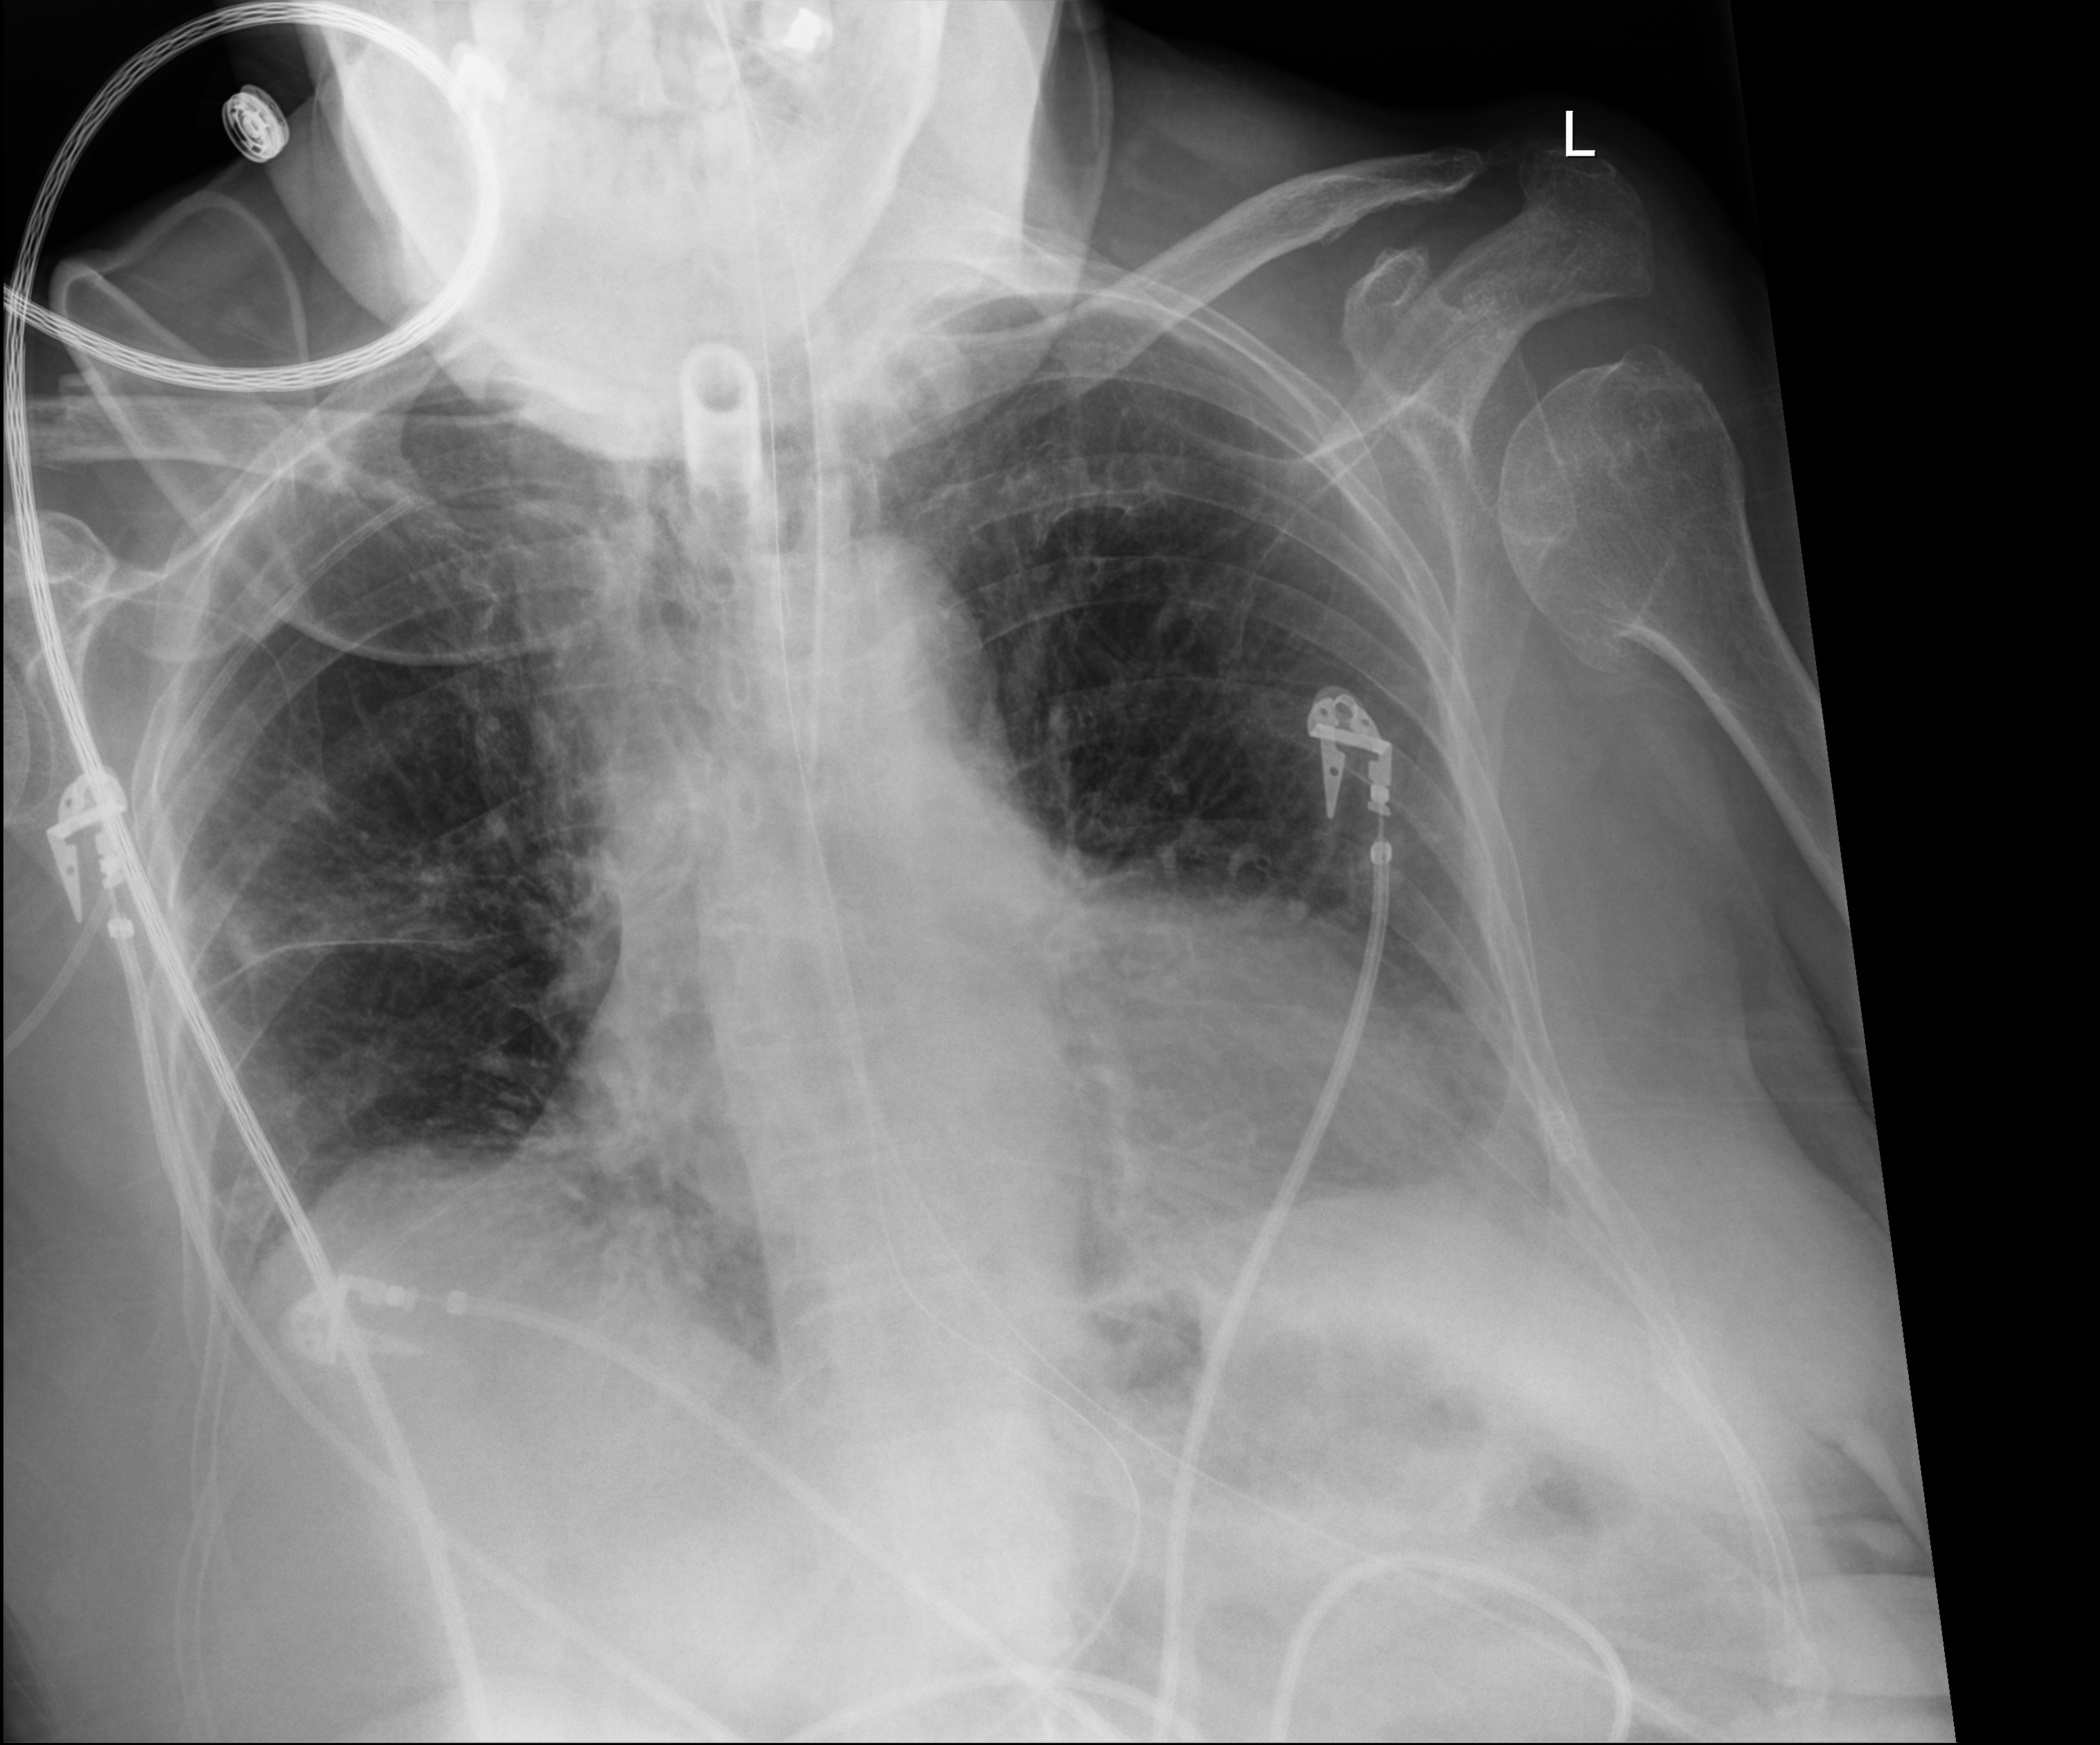
Portable chest radiograph. Female patient hospitalised with COVID-19, age 75–90 years.
Hospital-stay facts (about this admission, not read from this image; timing relative to this image not recorded): admitted to intensive care during this hospital stay: yes; mechanically ventilated during this hospital stay: yes; chronic kidney disease (admission record): yes.